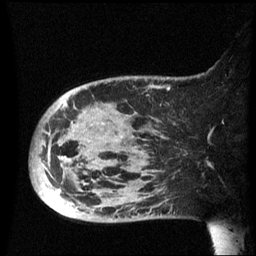
Breast MRI (dynamic contrast-enhanced), one sagittal slice; slice 16 of 60 in the series (ordered by position); dynamic contrast-enhanced series, image 2 of 3 at this slice position (ordered by acquisition); 1.5 T; TE 4.2 ms, TR 8.4 ms; 2.5 mm slice thickness; 256 × 256 image matrix, field of view 220 × 220 mm. Female patient, age 49 years.
Outlined on this slice (semi-automatically segmented with operator editing):
- analysis volume of interest (the breast-tissue region the enhancement analysis was run in; not a lesion): box from (x=30, y=76) to (x=184, y=223) px
- tumour enhancement mask (voxels above the 70 % enhancement threshold inside the analysis volume of interest): (x=48, y=104)–(x=68, y=167)